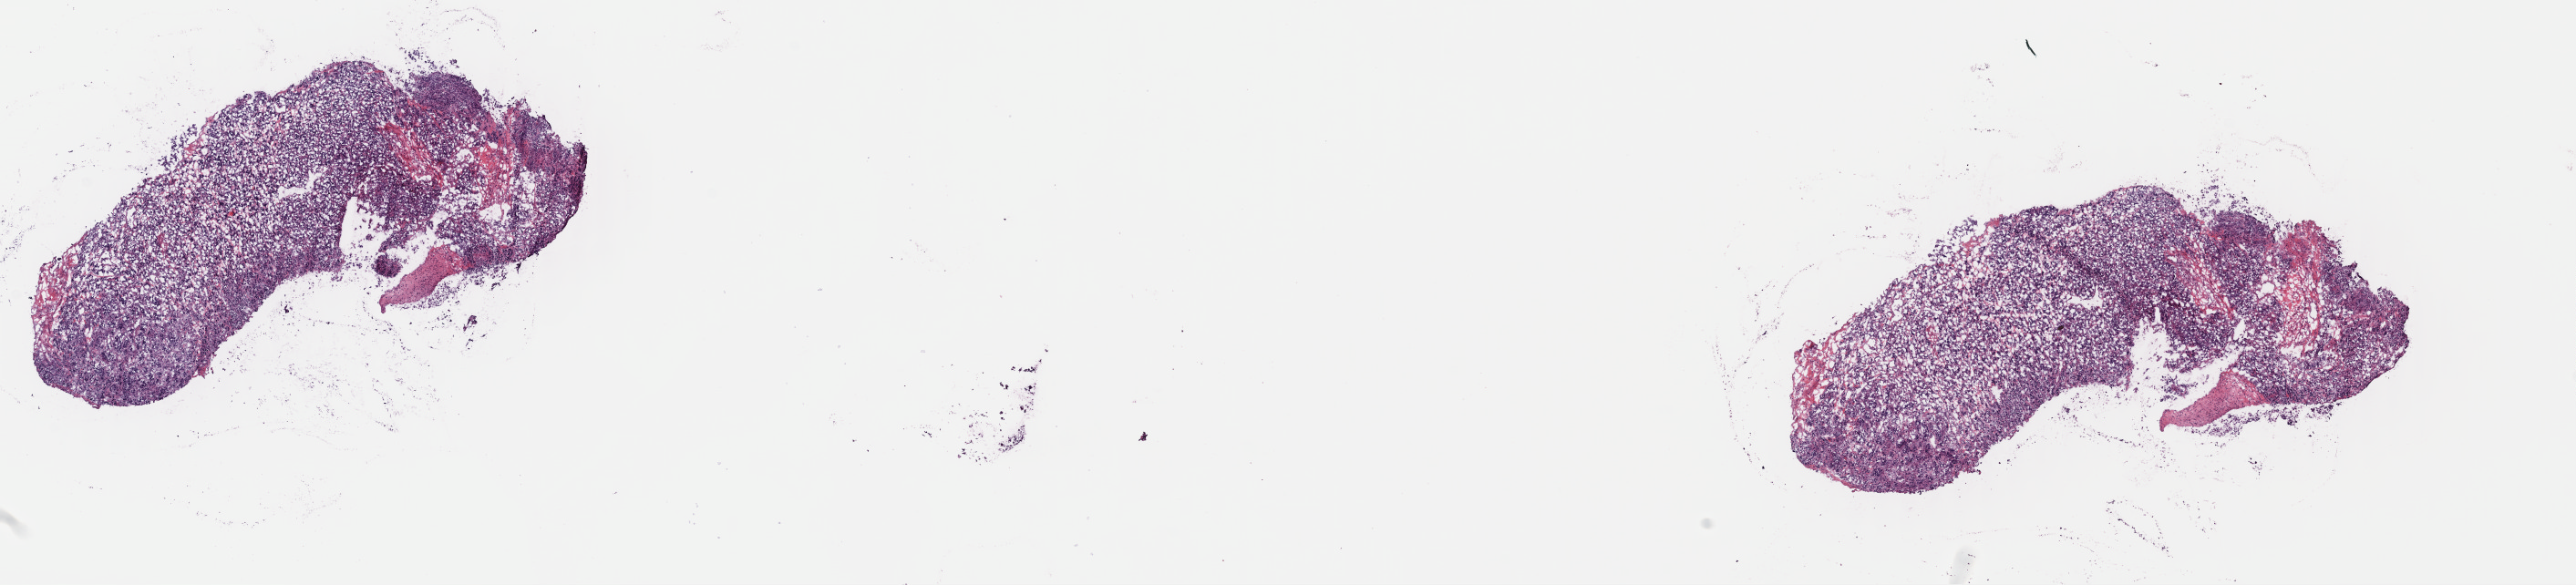
Digitized H&E-stained tissue section (whole slide) — shown as a low-resolution overview of the whole scanned area (about 22.2 x 5.0 mm, from a 40x scan); frozen section from the top of the tissue portion; adrenal gland, primary tumour sample. Male, age 26 years at initial diagnosis. Composition of this section per pathologist review: tumour cells 95%, tumour nuclei 90%, normal cells 0%, stromal cells 5%, necrosis 0%. Inflammatory infiltration, as recorded: lymphocyte infiltration 0%, monocyte infiltration 0%, neutrophil infiltration 0%.
* pathologic diagnosis: Pheochromocytoma, NOS